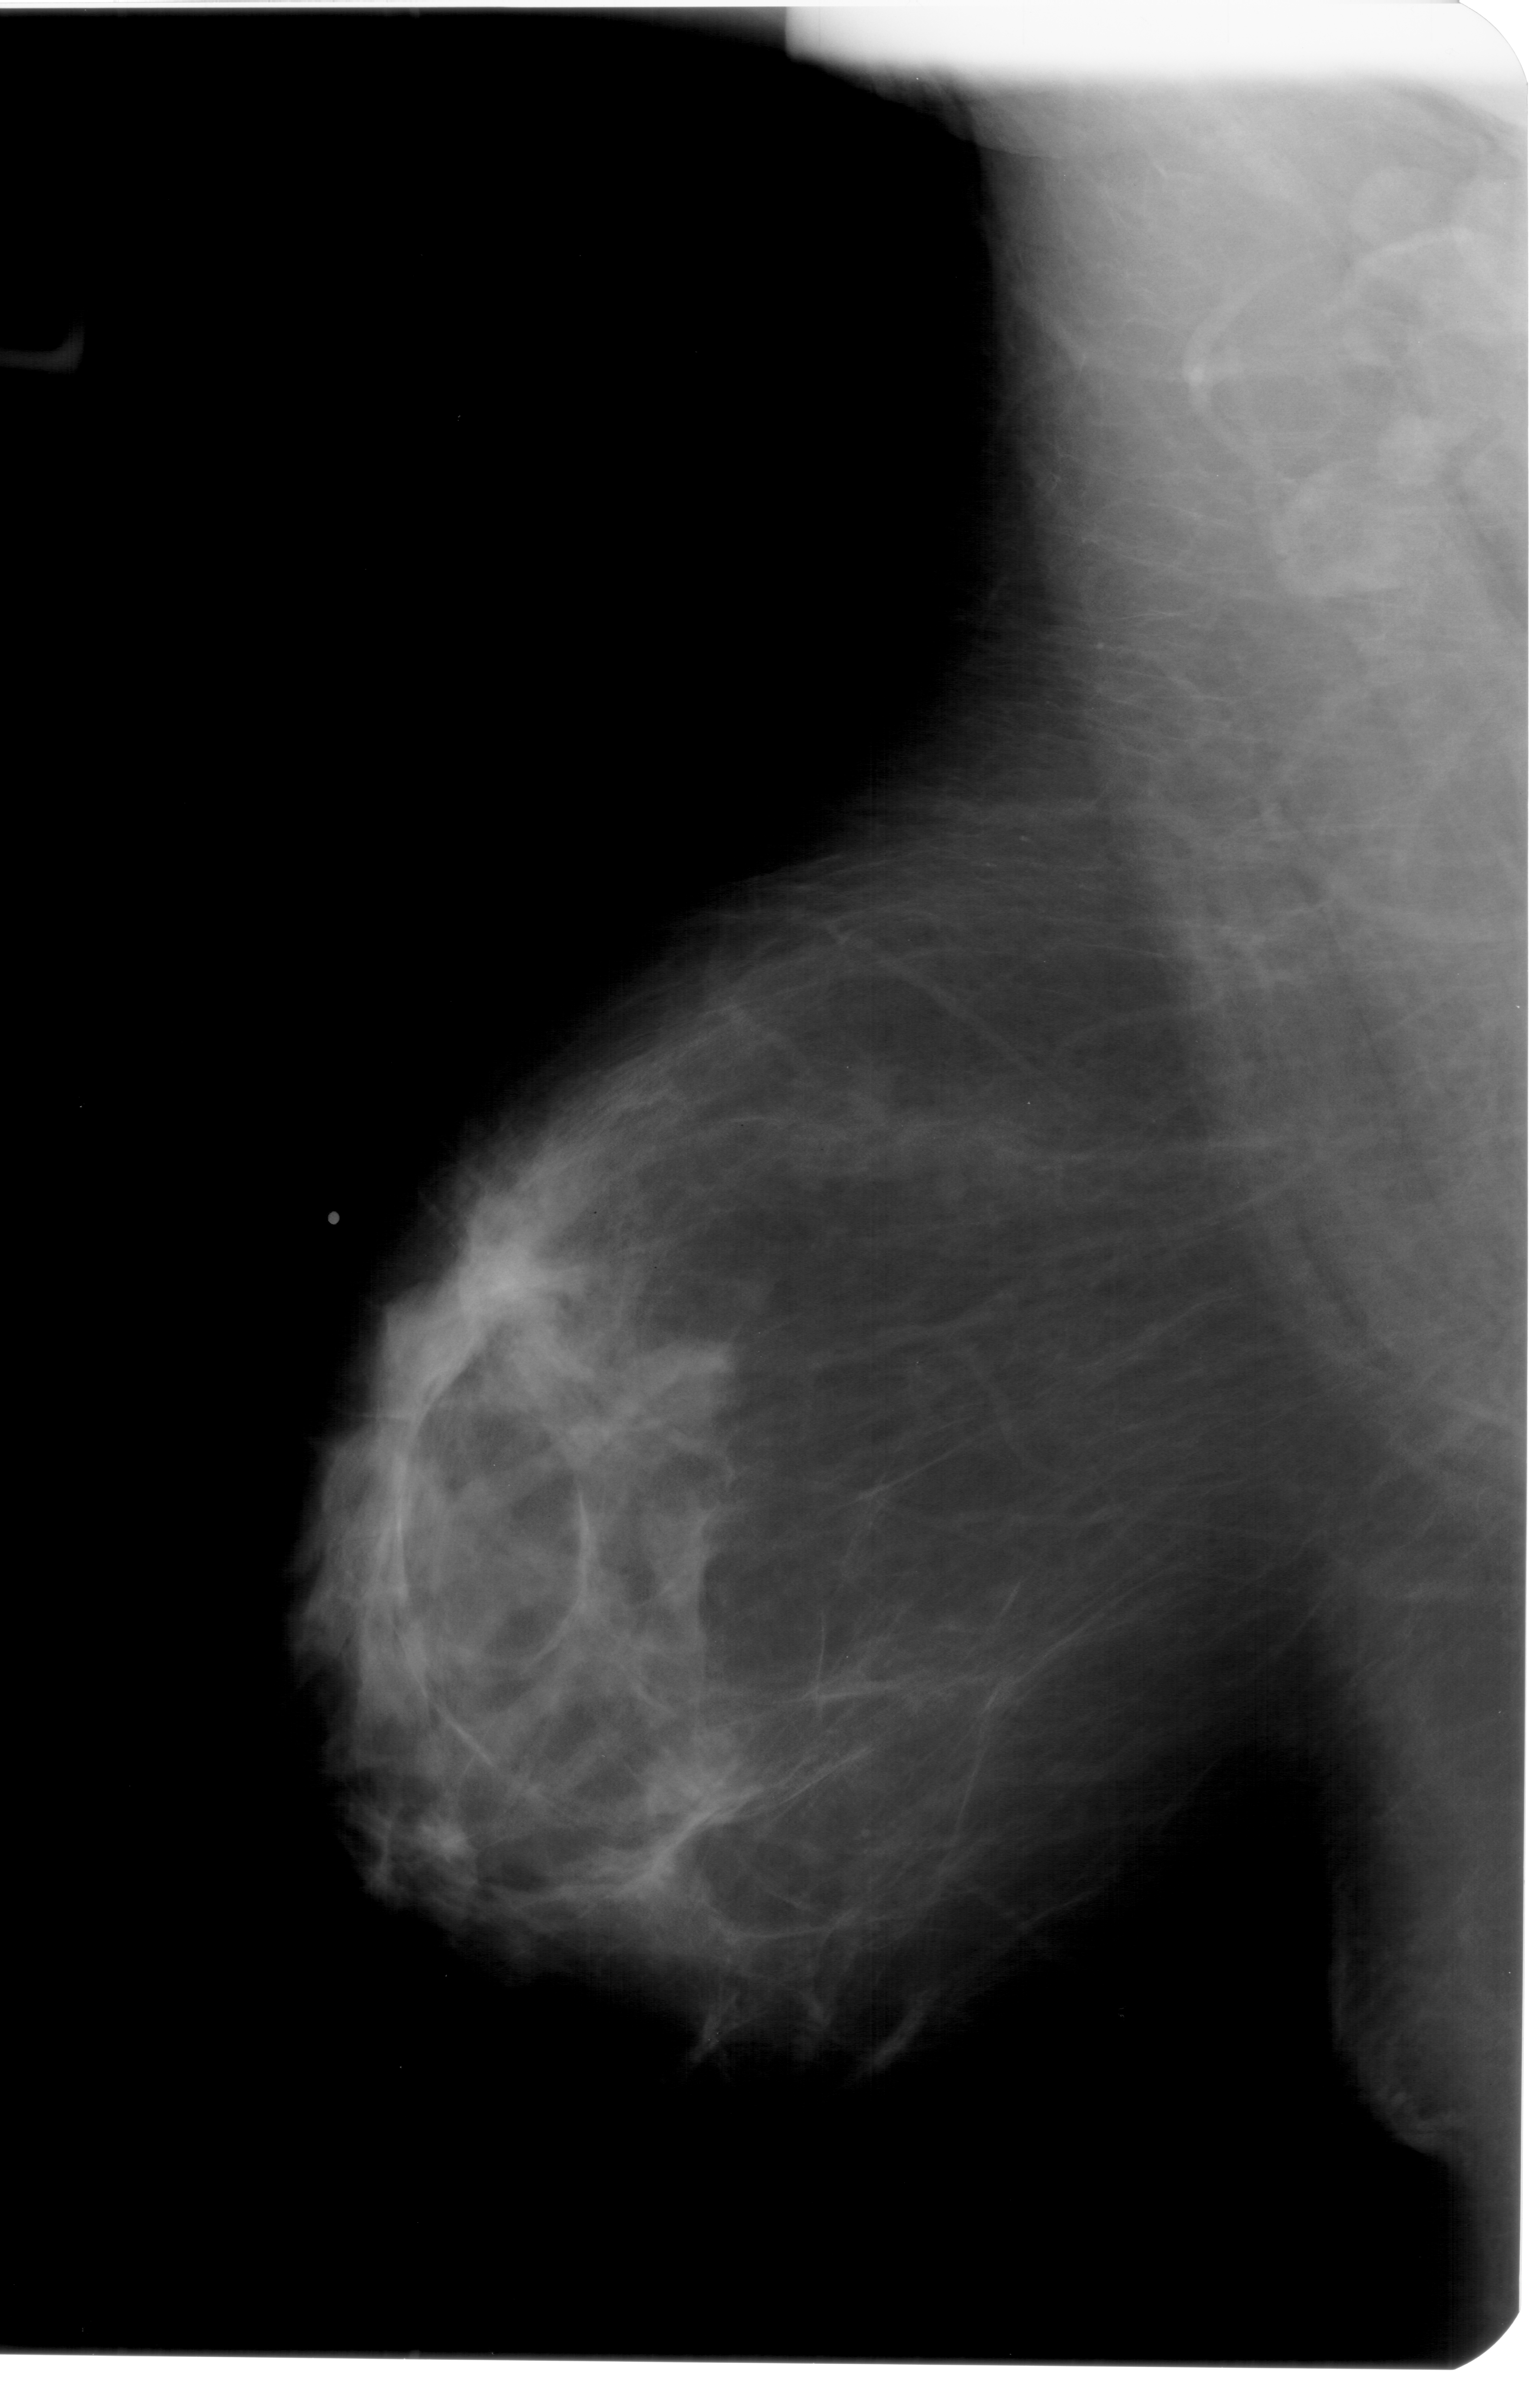
Digitized screen-film mammogram, left breast, mediolateral oblique (MLO) view, BI-RADS breast density category 1 (scale 1–4).
Marked abnormality: mass, shape irregular, margins spiculated; BI-RADS assessment category 5; pathology (as recorded): malignant.